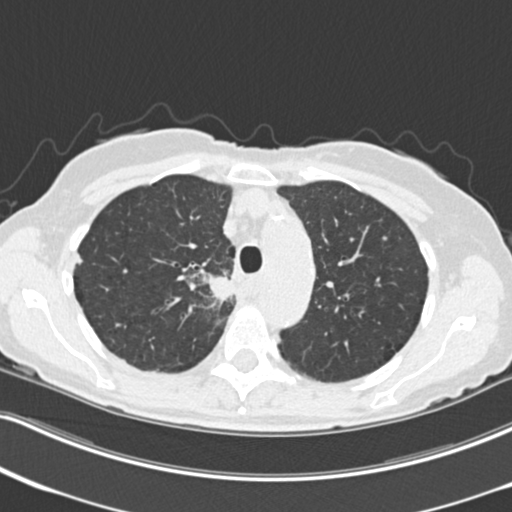
Low-dose screening chest CT, one axial slice; slice 168 of 226 in the series (ordered by position); reconstruction kernel B30f; 120 kVp; lung window (W 1500 / L -600 HU); 2 mm slice thickness; 512 × 512 image matrix, field of view 322 × 322 mm.
Structures marked on this image (expert manual segmentation):
- lesion 1 (tumor, mediastinum): bounding box [x1, y1, x2, y2] px = [209, 276, 233, 301]